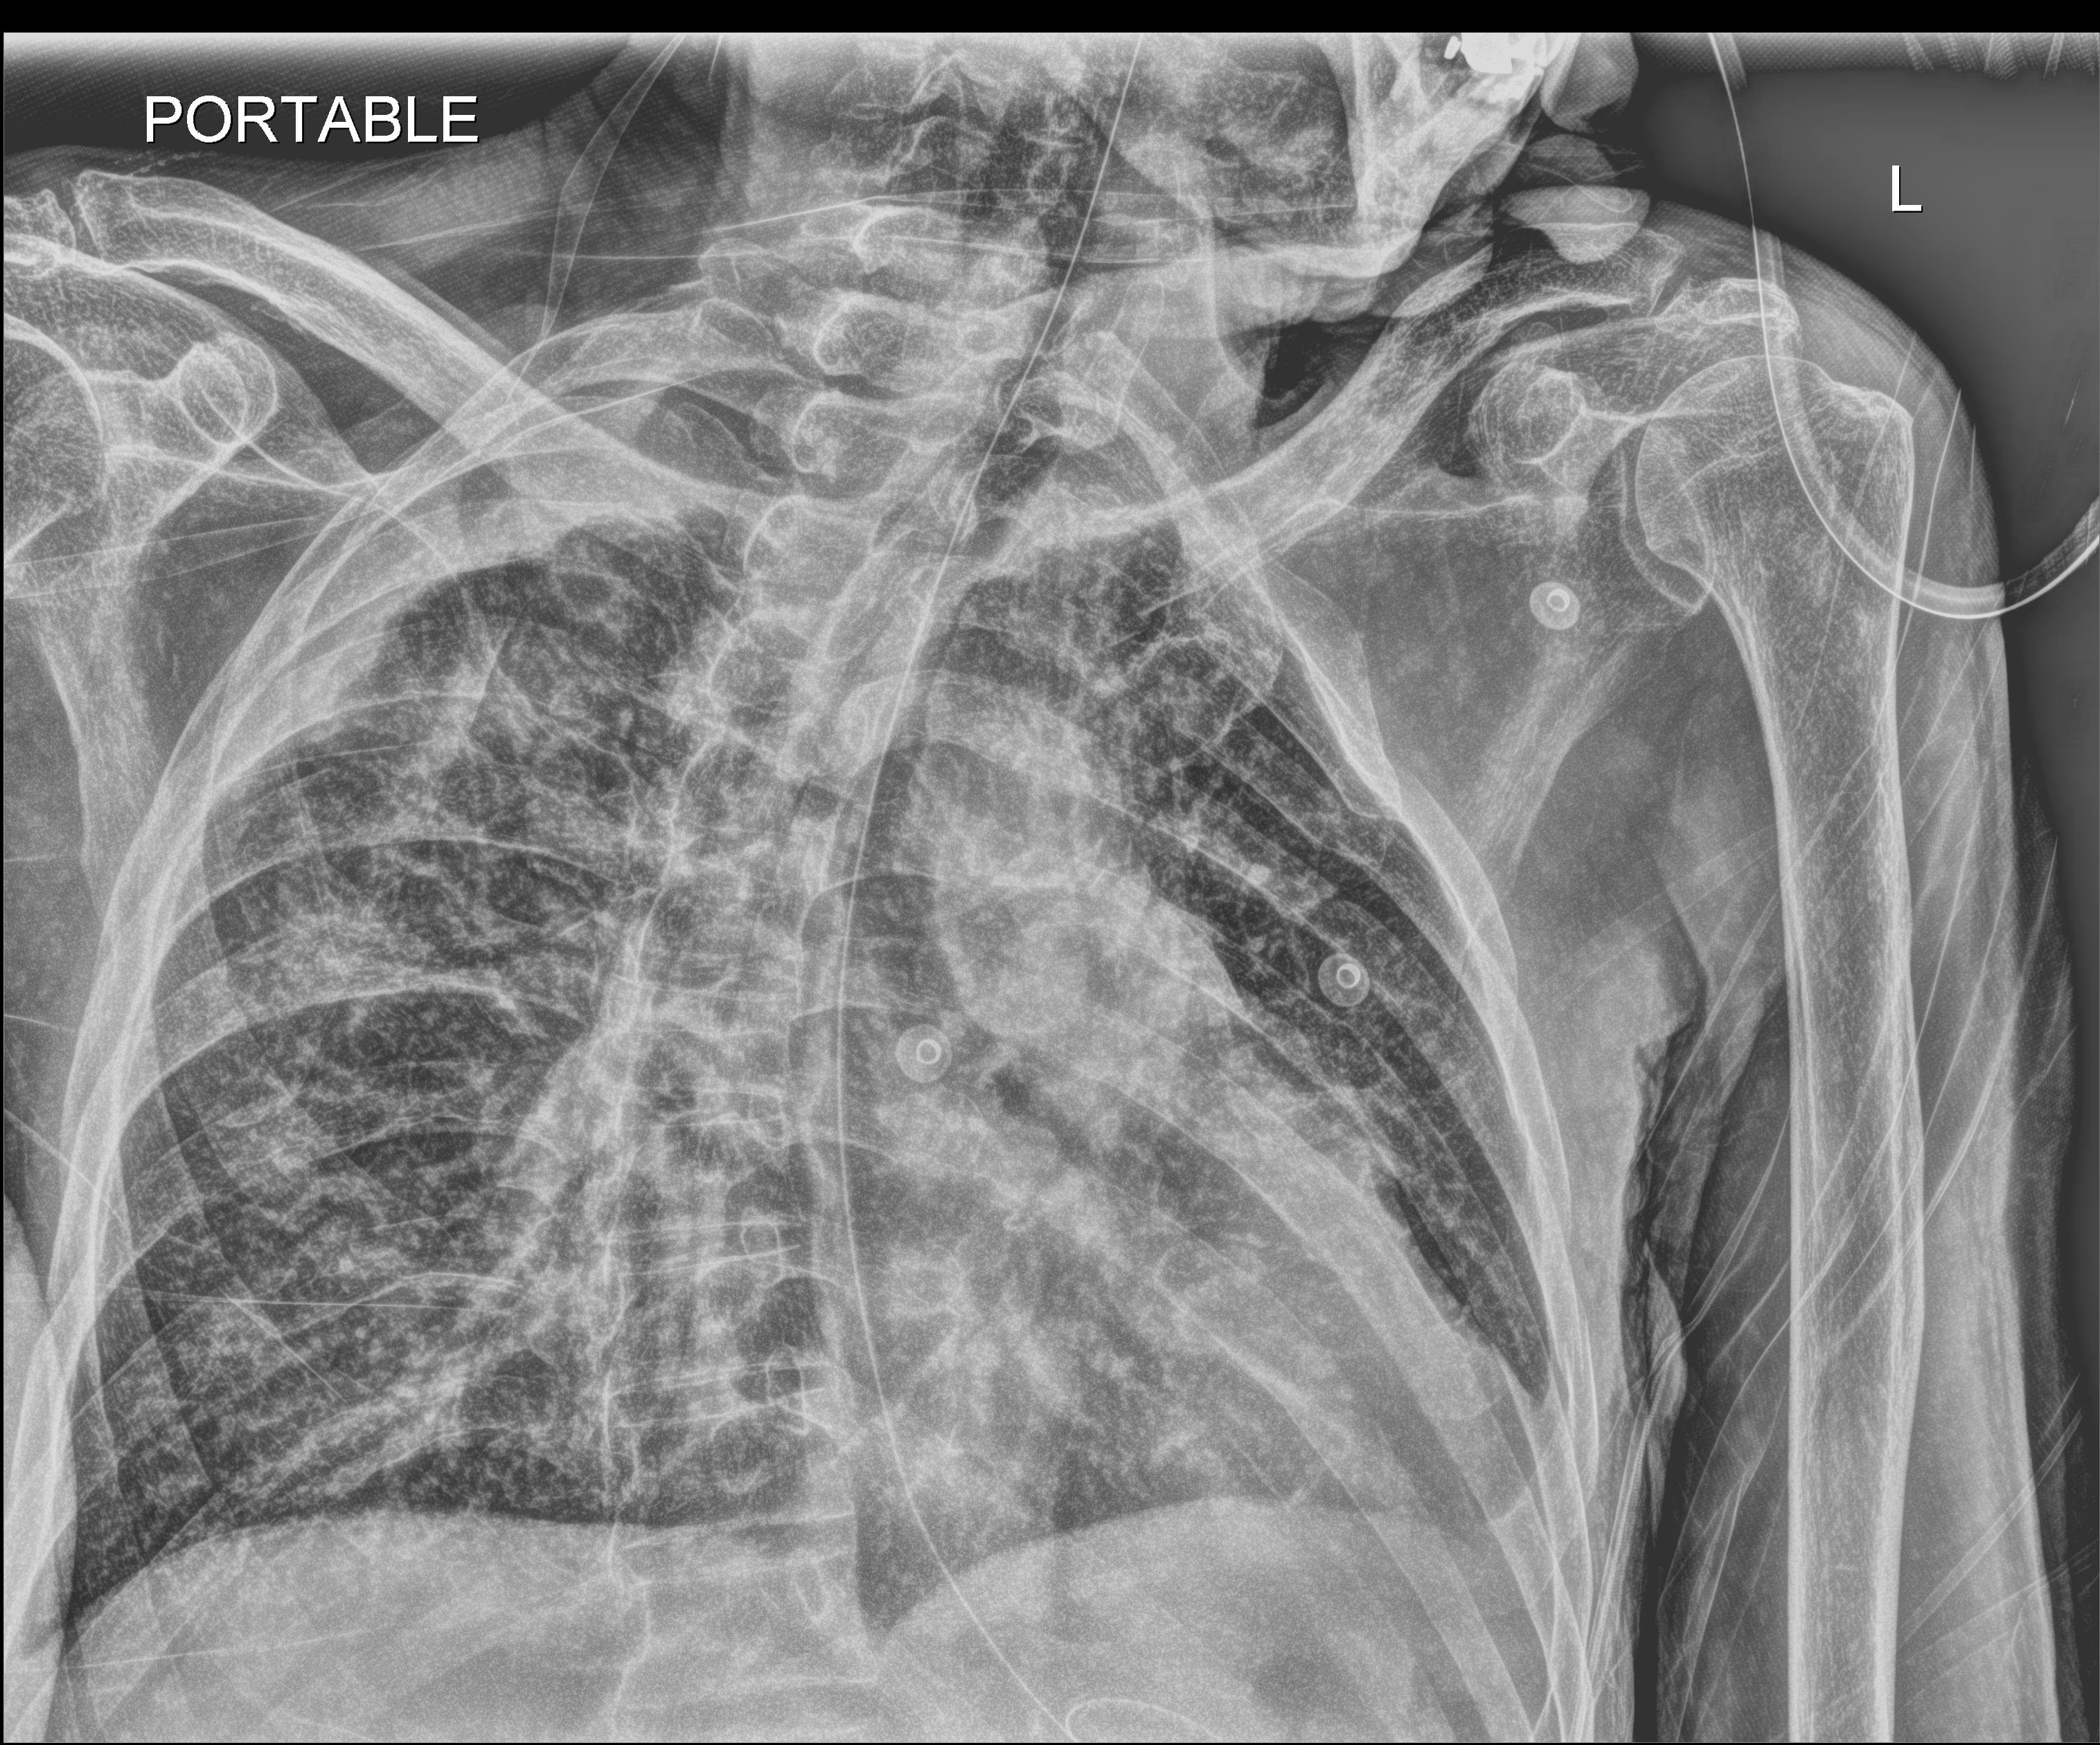
Bedside chest radiograph (digital radiography); anteroposterior (AP) projection. Male patient hospitalised with COVID-19, age 75–90 years.
Hospital-stay facts (about this admission, not read from this image; timing relative to this image not recorded): mechanically ventilated during this hospital stay: no.